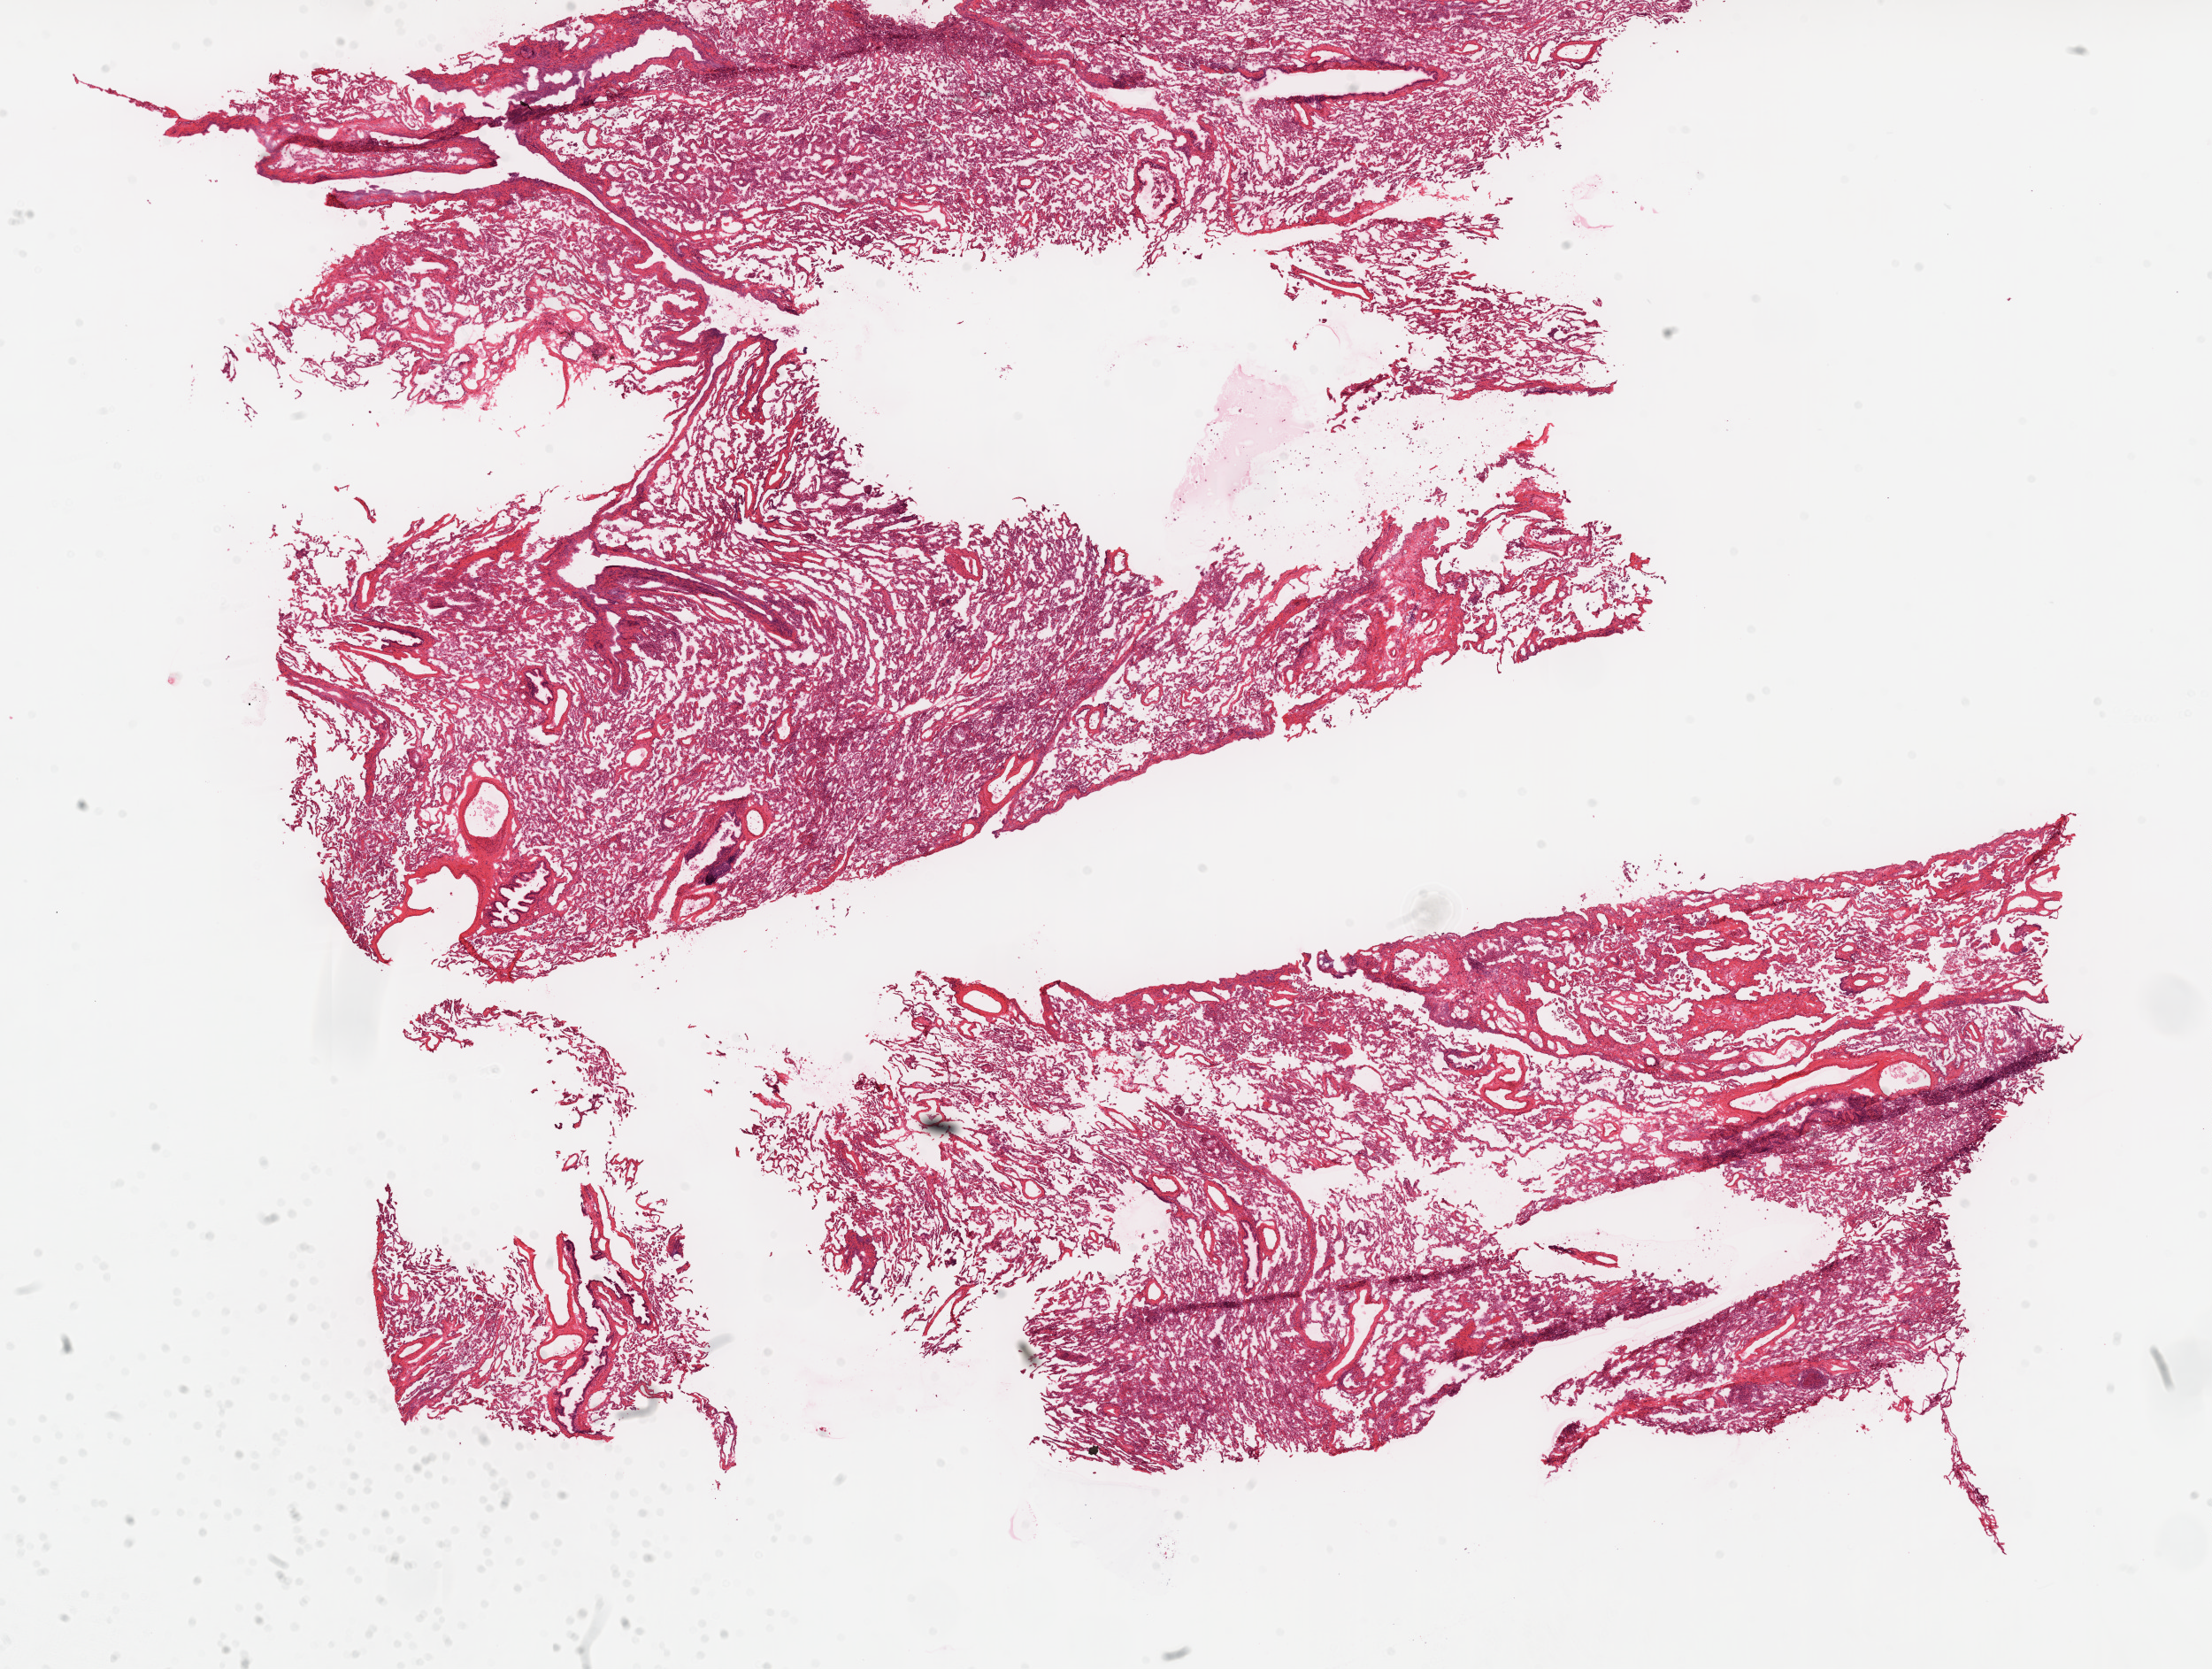
Whole-slide histology image, H&E-stained, low-resolution overview of the scanned area, about 20.1 x 15.1 mm (slide scanned at 20x); frozen section; lung, solid tissue normal (non-tumour tissue) sample. Patient: female, age at initial diagnosis 65 years.
This section: solid tissue normal (non-tumour) sample from the same patient. Patient diagnosis: Squamous cell carcinoma, NOS.